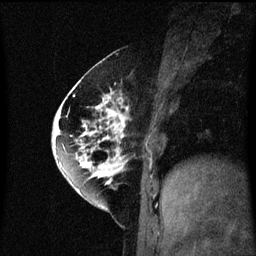
Breast MRI (dynamic contrast-enhanced), one sagittal slice; dynamic contrast-enhanced series, image 2 of 3 at this slice position (ordered by acquisition); 1.5 T; TE 4.2 ms, TR 8.4 ms; 256 × 256 image matrix, field of view 200 × 200 mm. Female patient, age 60 years.
Structures marked on this image (semi-automatic segmentation, software-assisted and operator-edited):
- analysis volume of interest (the breast-tissue region the enhancement analysis was run in; not a lesion): box from (x=64, y=70) to (x=133, y=195) px
- tumour enhancement mask (voxels above the 70 % enhancement threshold inside the analysis volume of interest): (x=64, y=78)–(x=129, y=193)